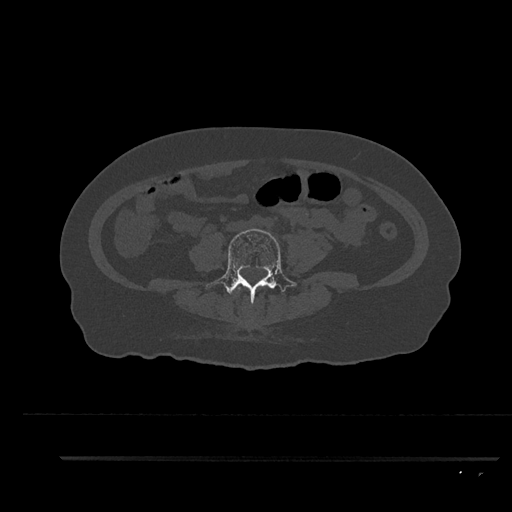
CT including the spine, one axial slice. Slice 29 of 797 in the series (ordered by position). Reconstruction kernel Br40s/3. 120 kVp. Bone window (W 1800 / L 400 HU). 0.5 mm slice thickness. 512 × 512 image matrix, field of view 408 × 408 mm. Patient: female, 44 years. From the clinical record (not read from this slice): primary cancer: renal; vertebrae with lytic lesions (as recorded): L1.
Structures marked on this image (semi-automatically segmented with operator editing):
- L3 vertebra: bounding box (x1, y1, x2, y2) in pixels: (234, 287, 241, 291)
- L4 vertebra: (206, 228, 297, 305)